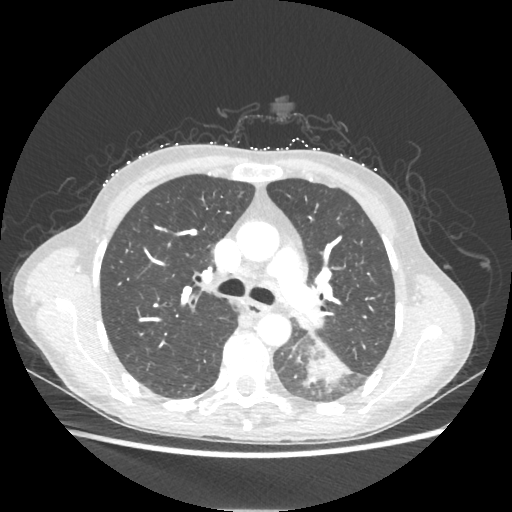
Chest CT, one axial slice; 80 kVp; lung window (W 1500 / L -600 HU); 1.25 mm slice thickness; 512 × 512 image matrix. Patient: female, 53 years. From the clinical record (not read from this slice): clinical TNM (as recorded): T3 N0 M0.
Annotated regions visible in this slice (rectangle marked by the reading radiologist):
- lung tumour (recorded histology: adenocarcinoma): bounding box [x1, y1, x2, y2] px = [308, 340, 348, 381]